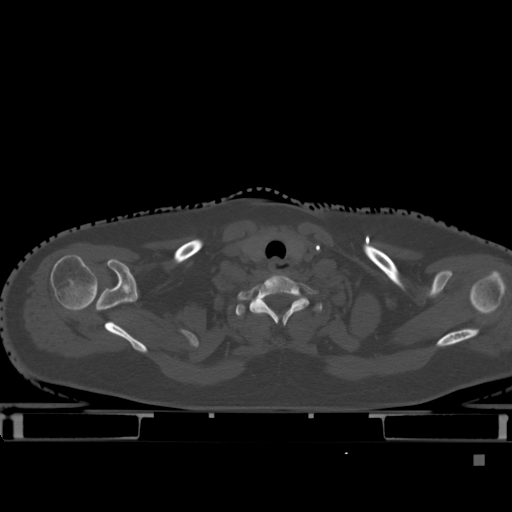
CT including the spine, one axial slice. Slice 378 of 495 in the series (ordered by position). Bone window (W 1800 / L 400 HU). 512 × 512 image matrix, field of view 404 × 404 mm. Patient: female, 33 years. Case-level facts recorded for this patient, not image findings: primary cancer: breast.
Structures marked on this image (semi-automatic segmentation, software-assisted and operator-edited):
- T1 vertebra: box from (x=235, y=297) to (x=323, y=324) px